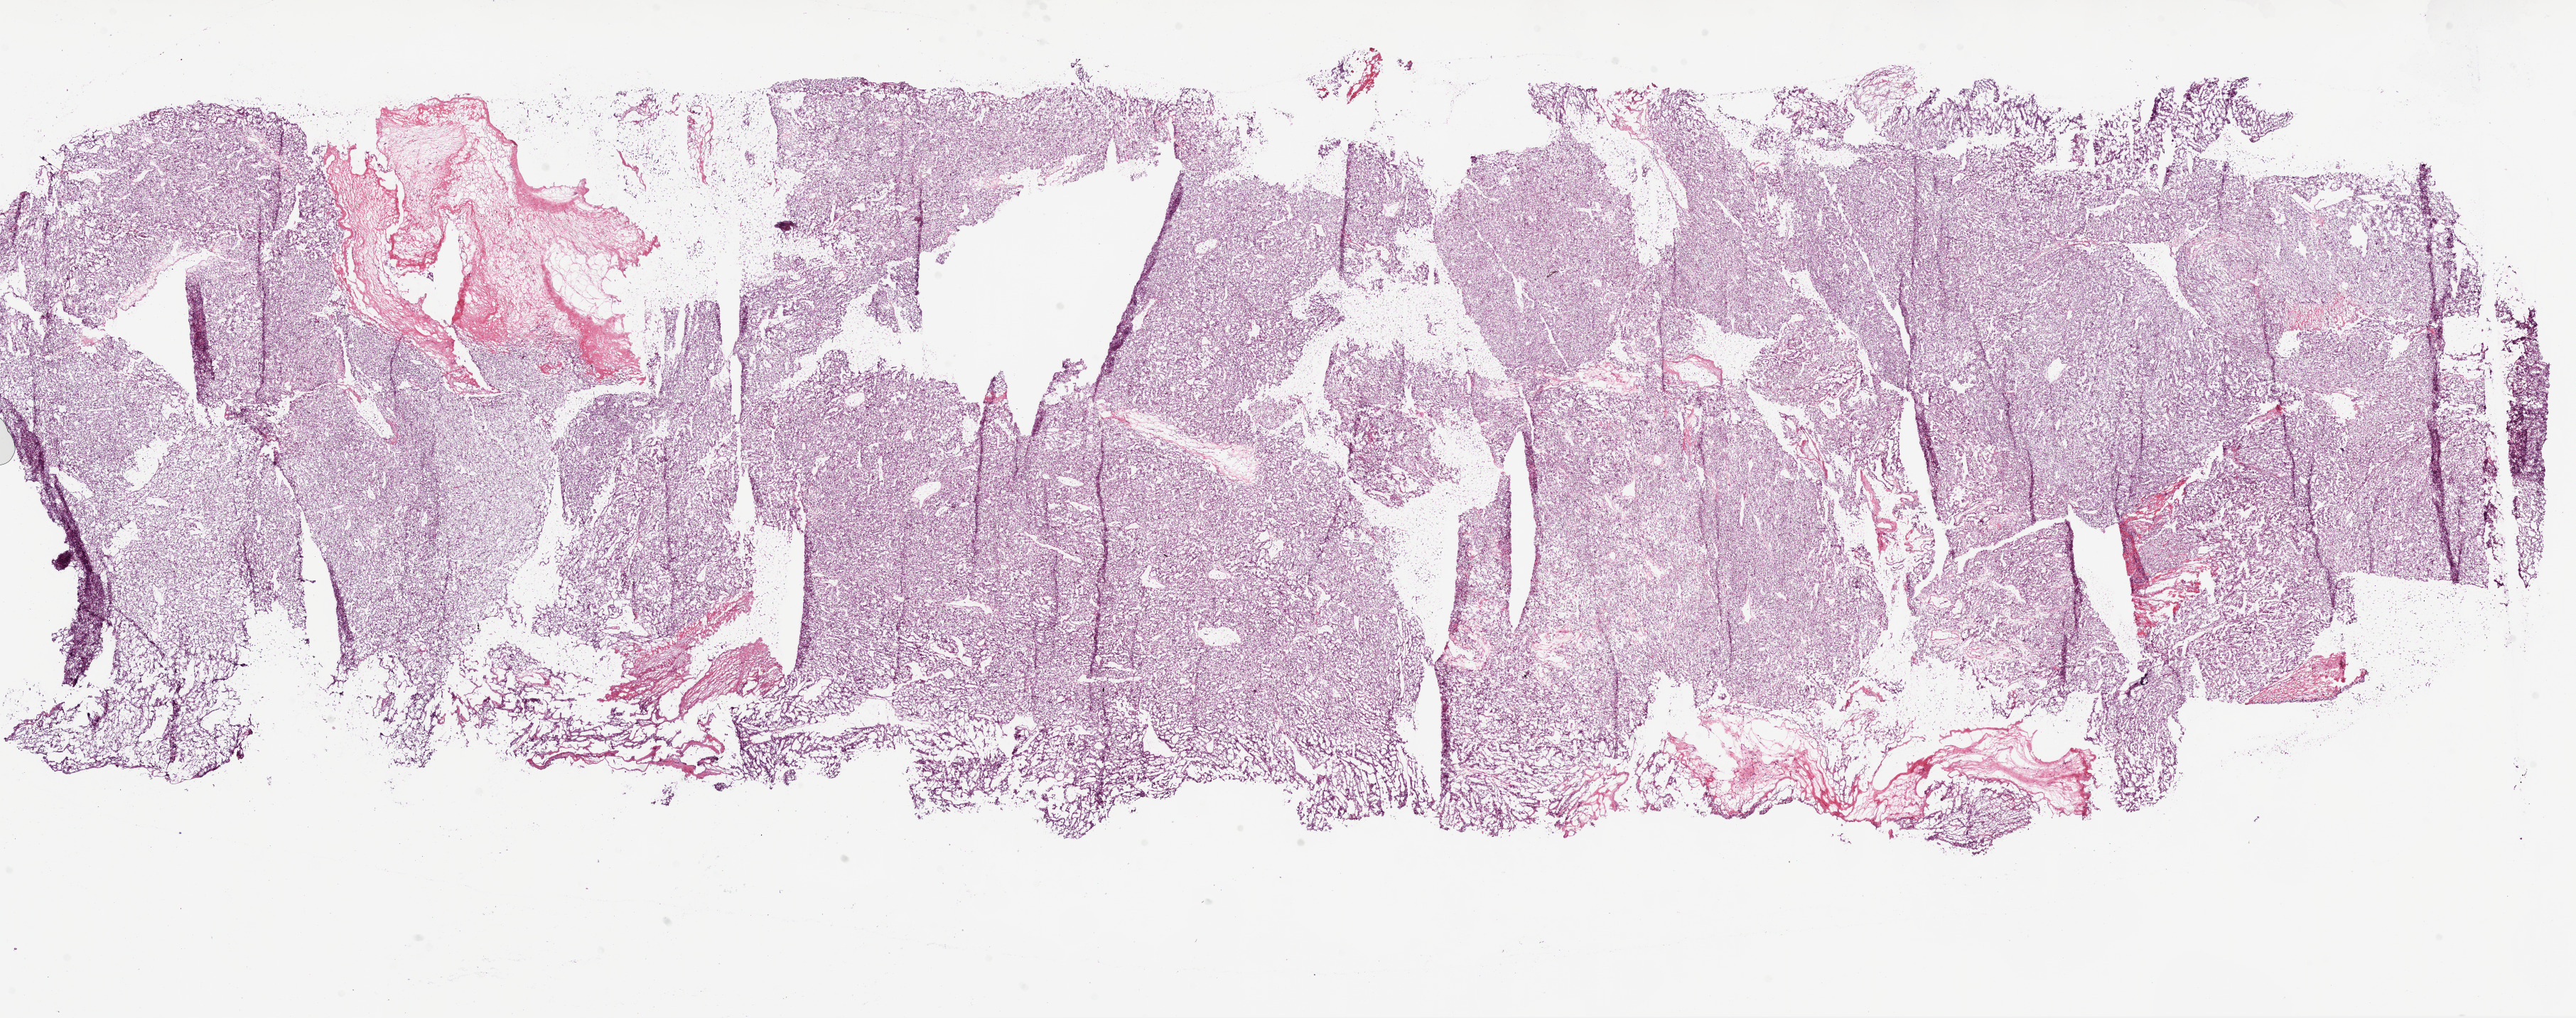
H&E-stained whole-slide image — shown as a low-resolution overview of the whole scanned area (about 29.1 x 11.5 mm); frozen section from the bottom of the tissue portion; primary tumour sample from the kidney. Male, age 67 years at initial diagnosis. Histologic grade: G3 (poorly differentiated). Pathologist review of this section (percent, as recorded): tumour cells 90%, tumour nuclei 90%, normal cells 0%, stromal cells 10%, necrosis 0%.
Histologic diagnosis: Clear cell adenocarcinoma, NOS. AJCC pathologic stage: IV. Laterality: right.